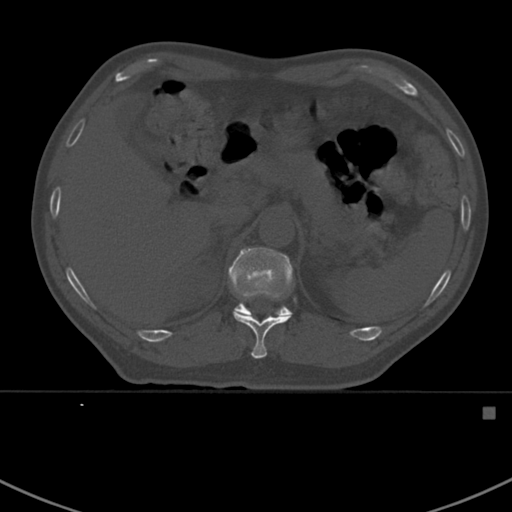
CT including the spine, one axial slice. Position 341 of 412 along the scan axis. Reconstruction kernel Br40s. Bone window (W 1800 / L 400 HU). 512 × 512 image matrix, field of view 358 × 358 mm. Male patient, age 59 years. From the clinical record (not read from this slice): primary cancer: prostate.
Structures marked on this image (semi-automatically segmented with operator editing):
- T11 vertebra: bounding box <234,313,292,359> (left, top, right, bottom; pixels)
- T12 vertebra: <228,246,293,316>